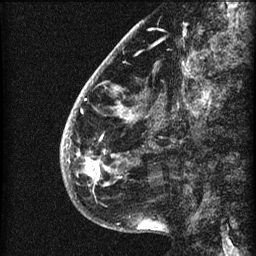
Breast MRI (dynamic contrast-enhanced), one sagittal slice. Position 17 of 60 along the scan axis. 3 images stored at this slice position (order not interpretable as contrast timing). 1.5 T. TE 4.2 ms, TR 22.7 ms. 2 mm slice thickness. 256 × 256 image matrix, field of view 180 × 180 mm. Patient: female, 48 years. From the clinical record (not read from this slice): setting: breast cancer imaged before/during neoadjuvant chemotherapy; receptor status: triple-negative.
Structures marked on this image (semi-automatic segmentation, software-assisted and operator-edited):
- analysis volume of interest (the breast-tissue region the enhancement analysis was run in; not a lesion): bounding box <61,30,173,207> (left, top, right, bottom; pixels)
- tumour enhancement mask (voxels above the 90 % enhancement threshold inside the analysis volume of interest): <62,99,124,186>